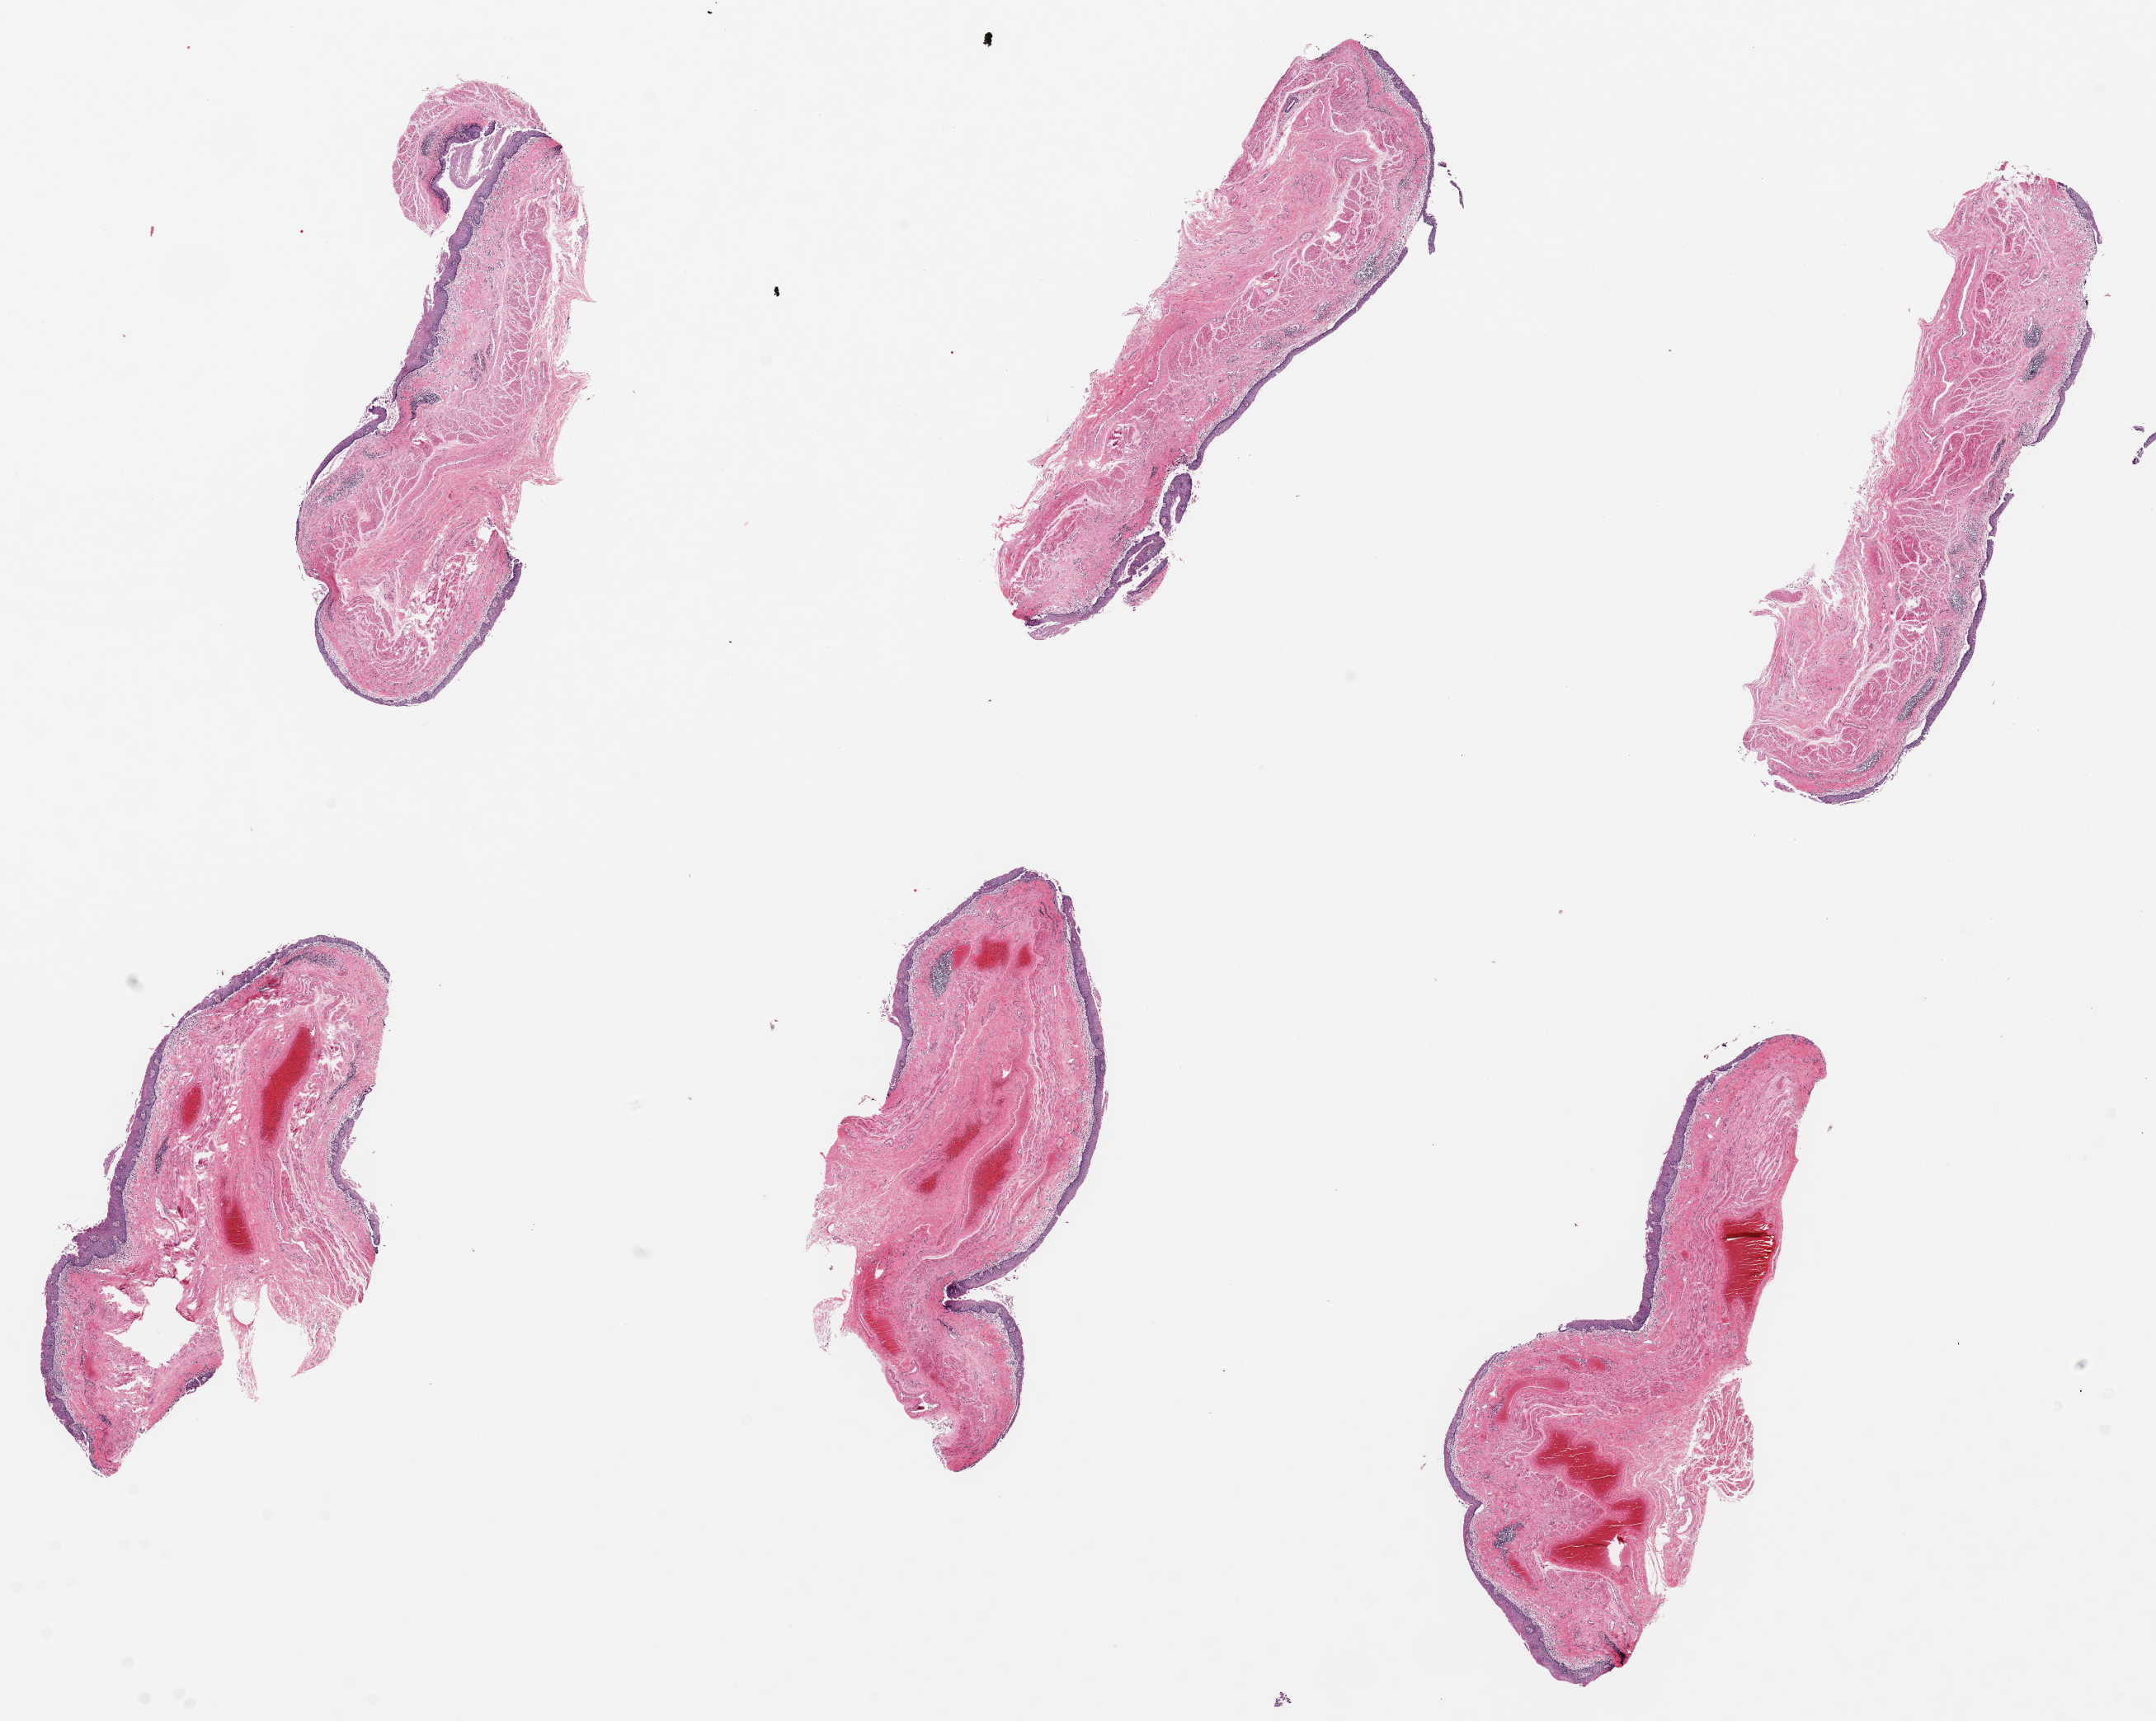
Digitized haematoxylin and eosin-stained section, brightfield, low-resolution overview of the scanned area, about 20.7 x 16.5 mm, PAXgene-fixed paraffin-embedded (PFPE) section, section of esophageal mucous membrane (target tissue), donor tissue sample.
- reviewer comment on this tissue sample: 6 pieces, up to 6x2mm; epithelium partially sloughed